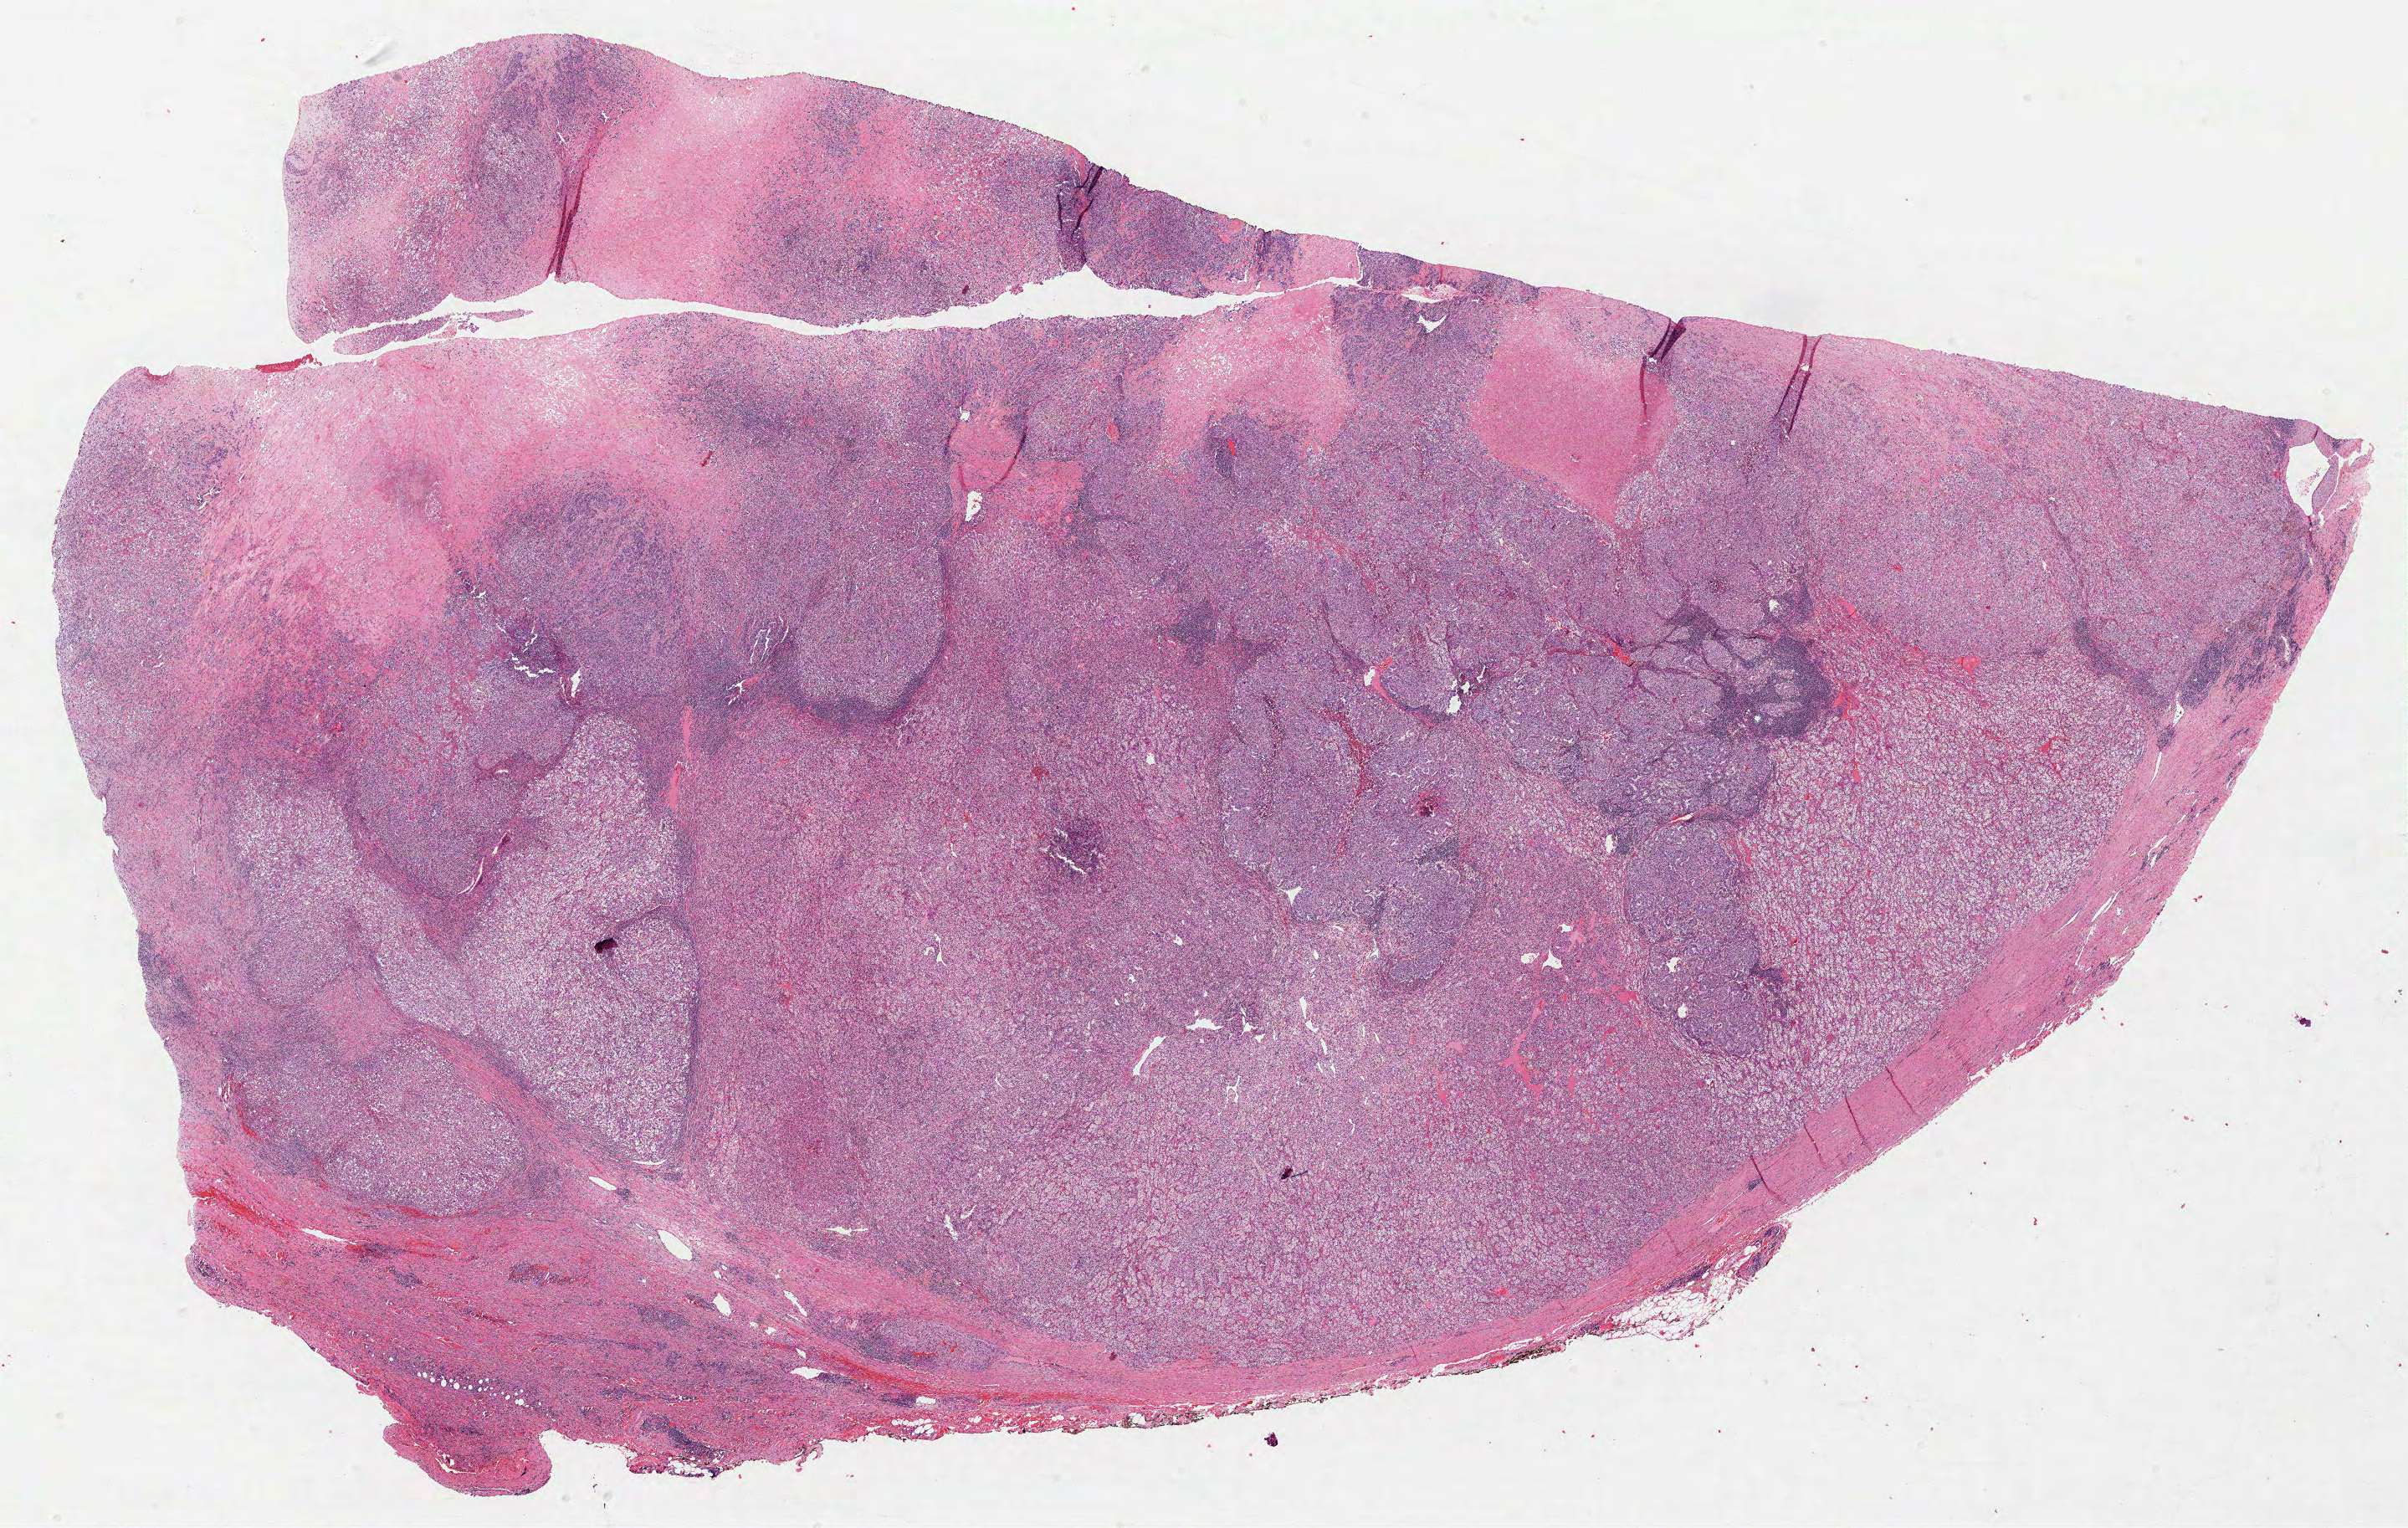
H&E whole-slide image, a low-resolution overview of the entire scanned area, about 23.2 x 14.7 mm; formalin-fixed paraffin-embedded (FFPE) diagnostic section; sample: primary tumour, kidney. Male, age 52 years at initial diagnosis. Histologic grade: G4 (undifferentiated).
Pathologic diagnosis: Clear cell adenocarcinoma, NOS. TNM: T1b NX M1. AJCC pathologic stage: IV. Laterality: right.